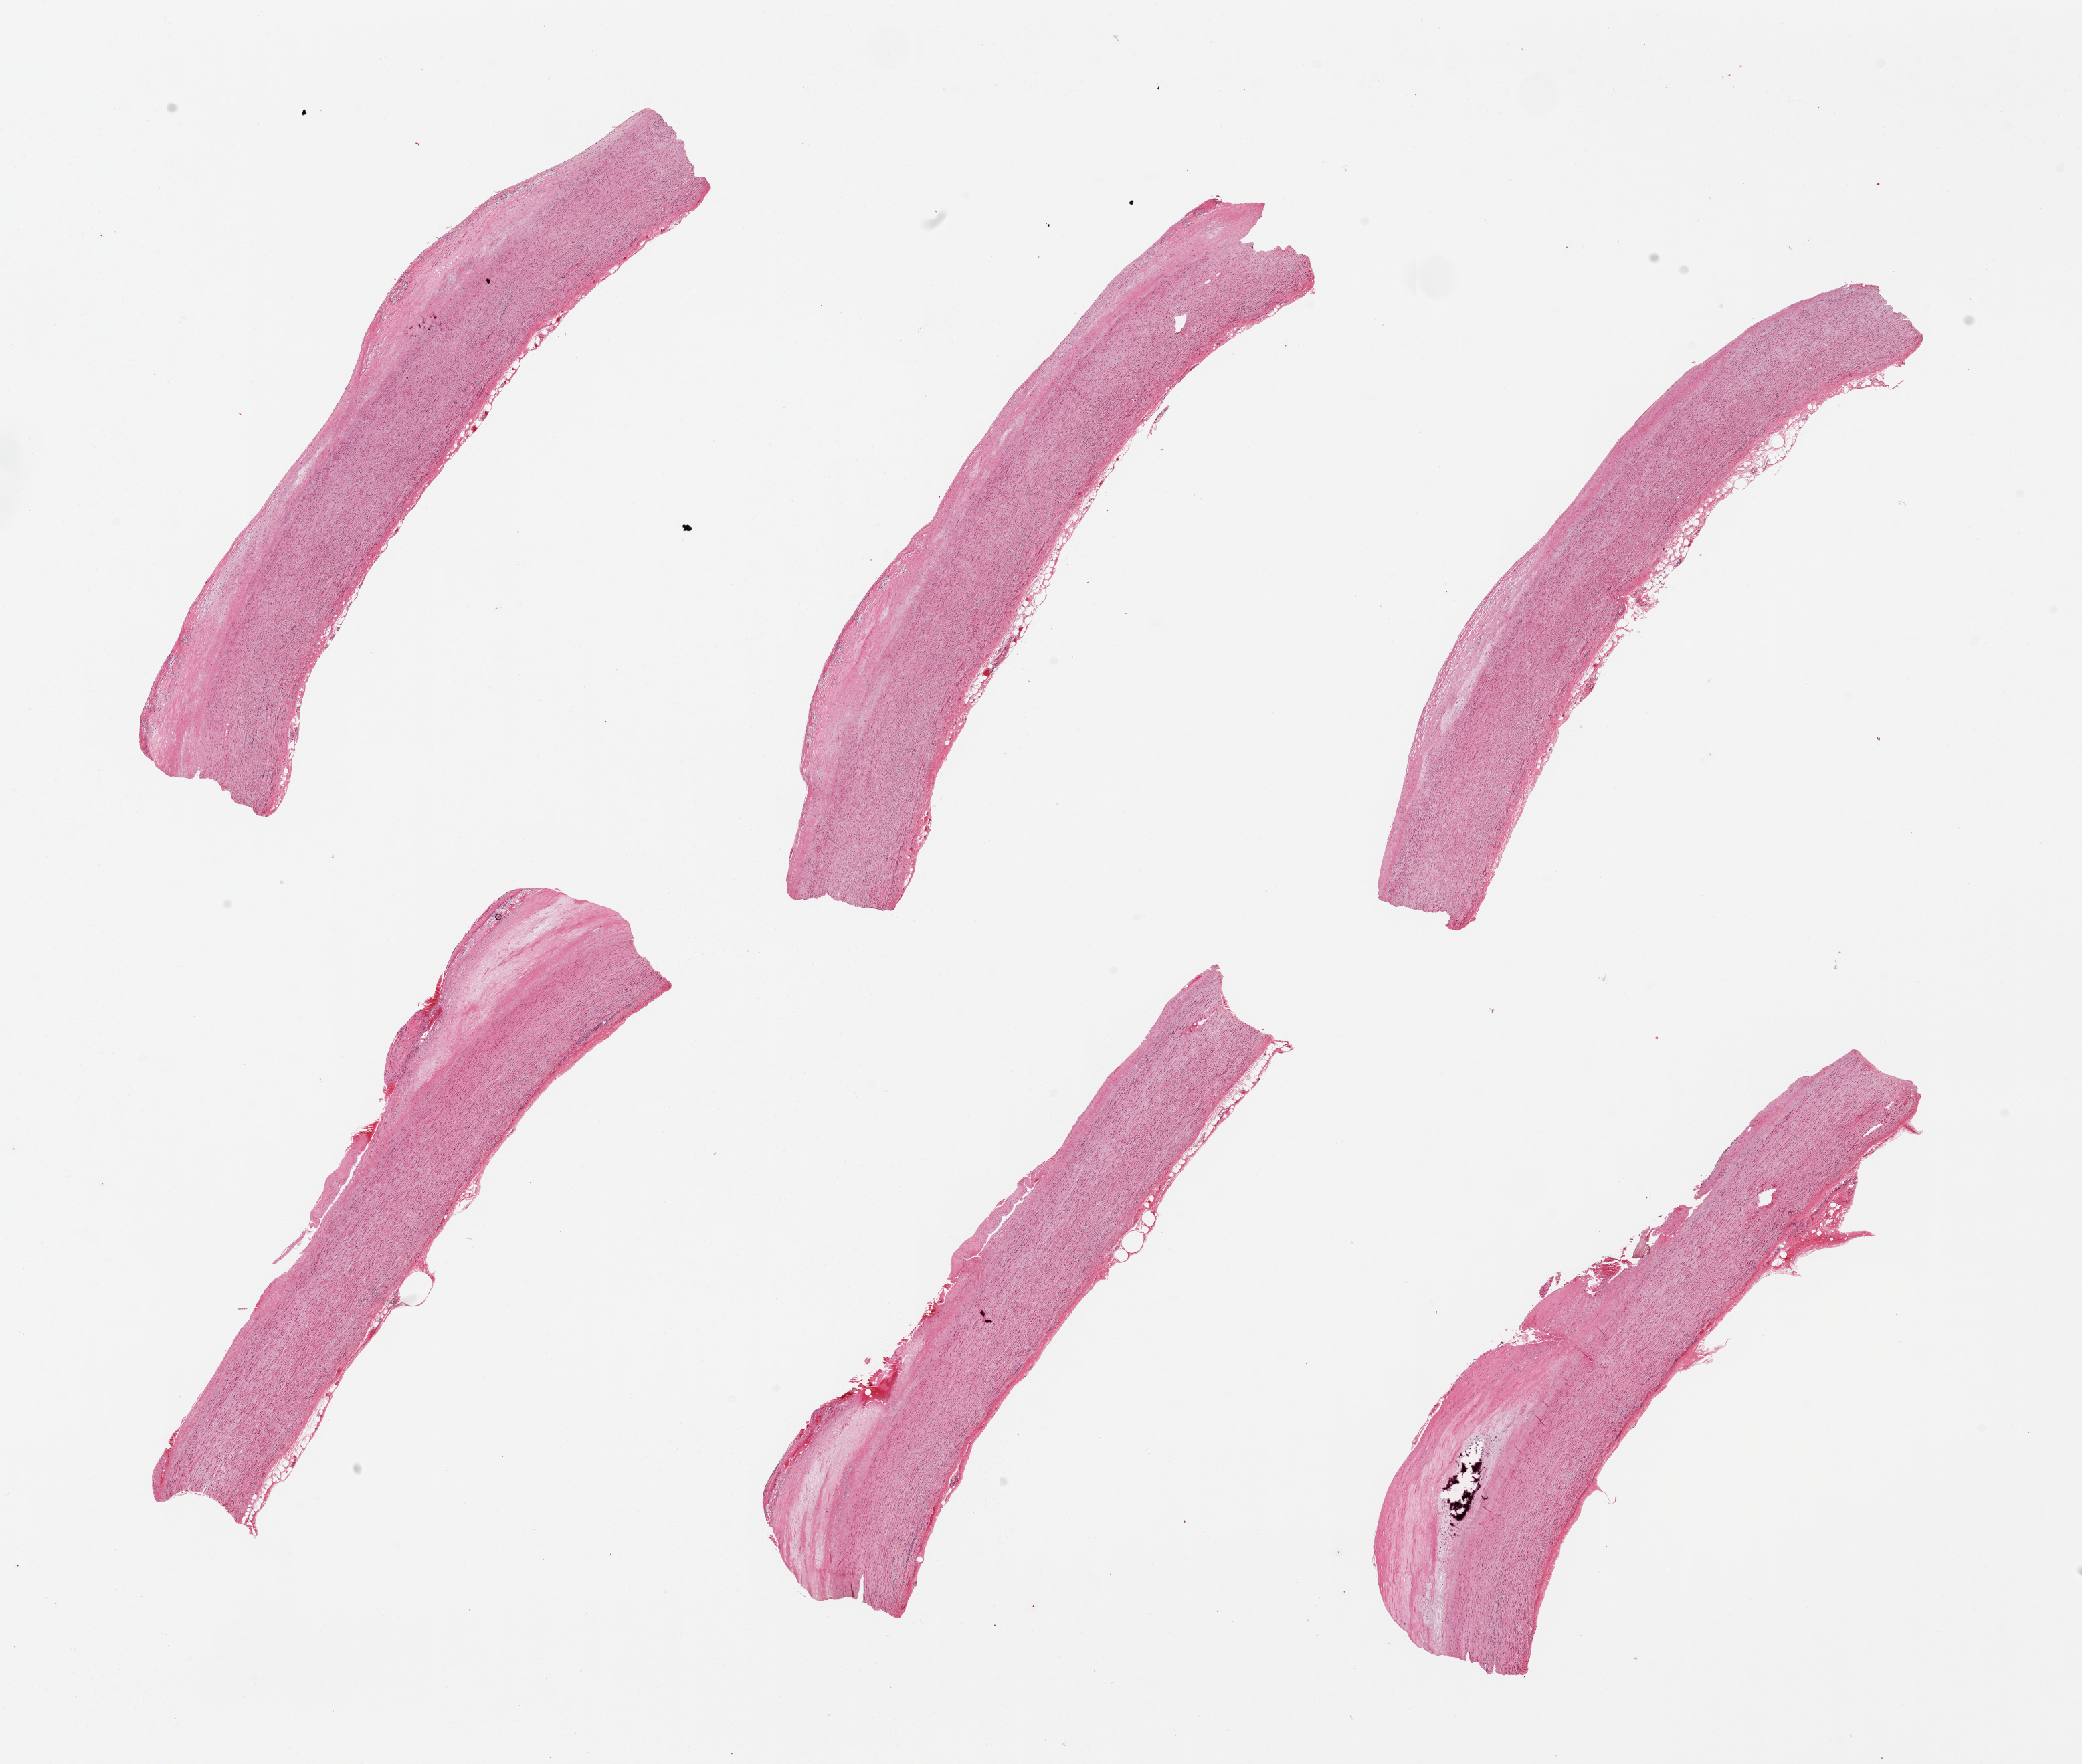
Digitized H&E-stained section — a low-resolution overview of the entire scanned area, about 24.6 x 20.9 mm, PAXgene-fixed paraffin-embedded (PFPE) section, sampled site (target tissue): aorta, donor tissue sample. Donor sex: male.
- pathologist's review note for this sample: 6 pieces, up to 10x2mm; marked focally calcified atherosis, focally calcified